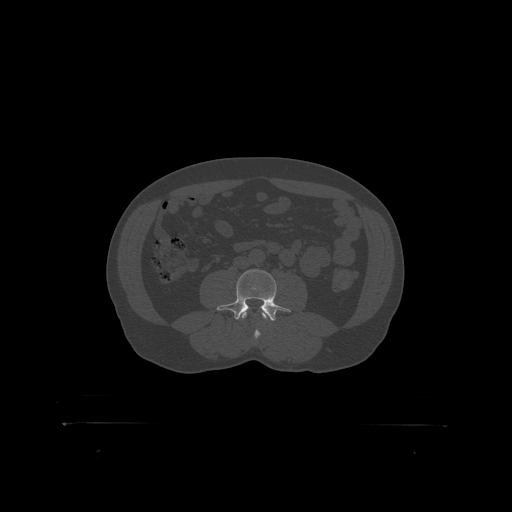
CT including the spine, one axial slice; position 244 of 399 along the scan axis; reconstruction kernel STANDARD; 120 kVp; bone window (W 1800 / L 400 HU); 512 × 512 image matrix. Patient: male, 46 years. Case-level facts recorded for this patient, not image findings: primary cancer: skin.
Outlined on this slice (semi-automatic segmentation, software-assisted and operator-edited):
- L3 vertebra: bounding box (x1, y1, x2, y2) in pixels: (242, 312, 267, 319)
- L4 vertebra: (219, 270, 289, 317)